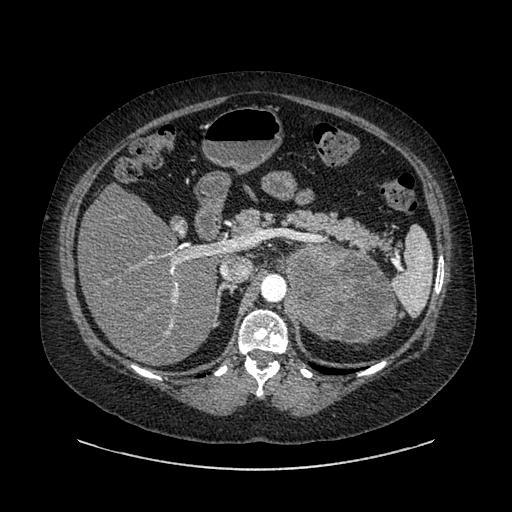
Contrast-enhanced abdominal CT, one axial slice. Slice 577 of 769 in the series (ordered by position). 120 kVp. Soft-tissue window (W 400 / L 40 HU). 0.62 mm slice thickness. 512 × 512 image matrix, field of view 460 × 460 mm. Patient: female, 61 years. From the clinical record (not read from this slice): diagnosis: adrenocortical carcinoma; tumour side: left adrenal; tumour size at pathology: 13 cm.
Outlined on this slice (semi-automatically segmented with operator editing):
- mass: box from (x=285, y=245) to (x=393, y=343) px